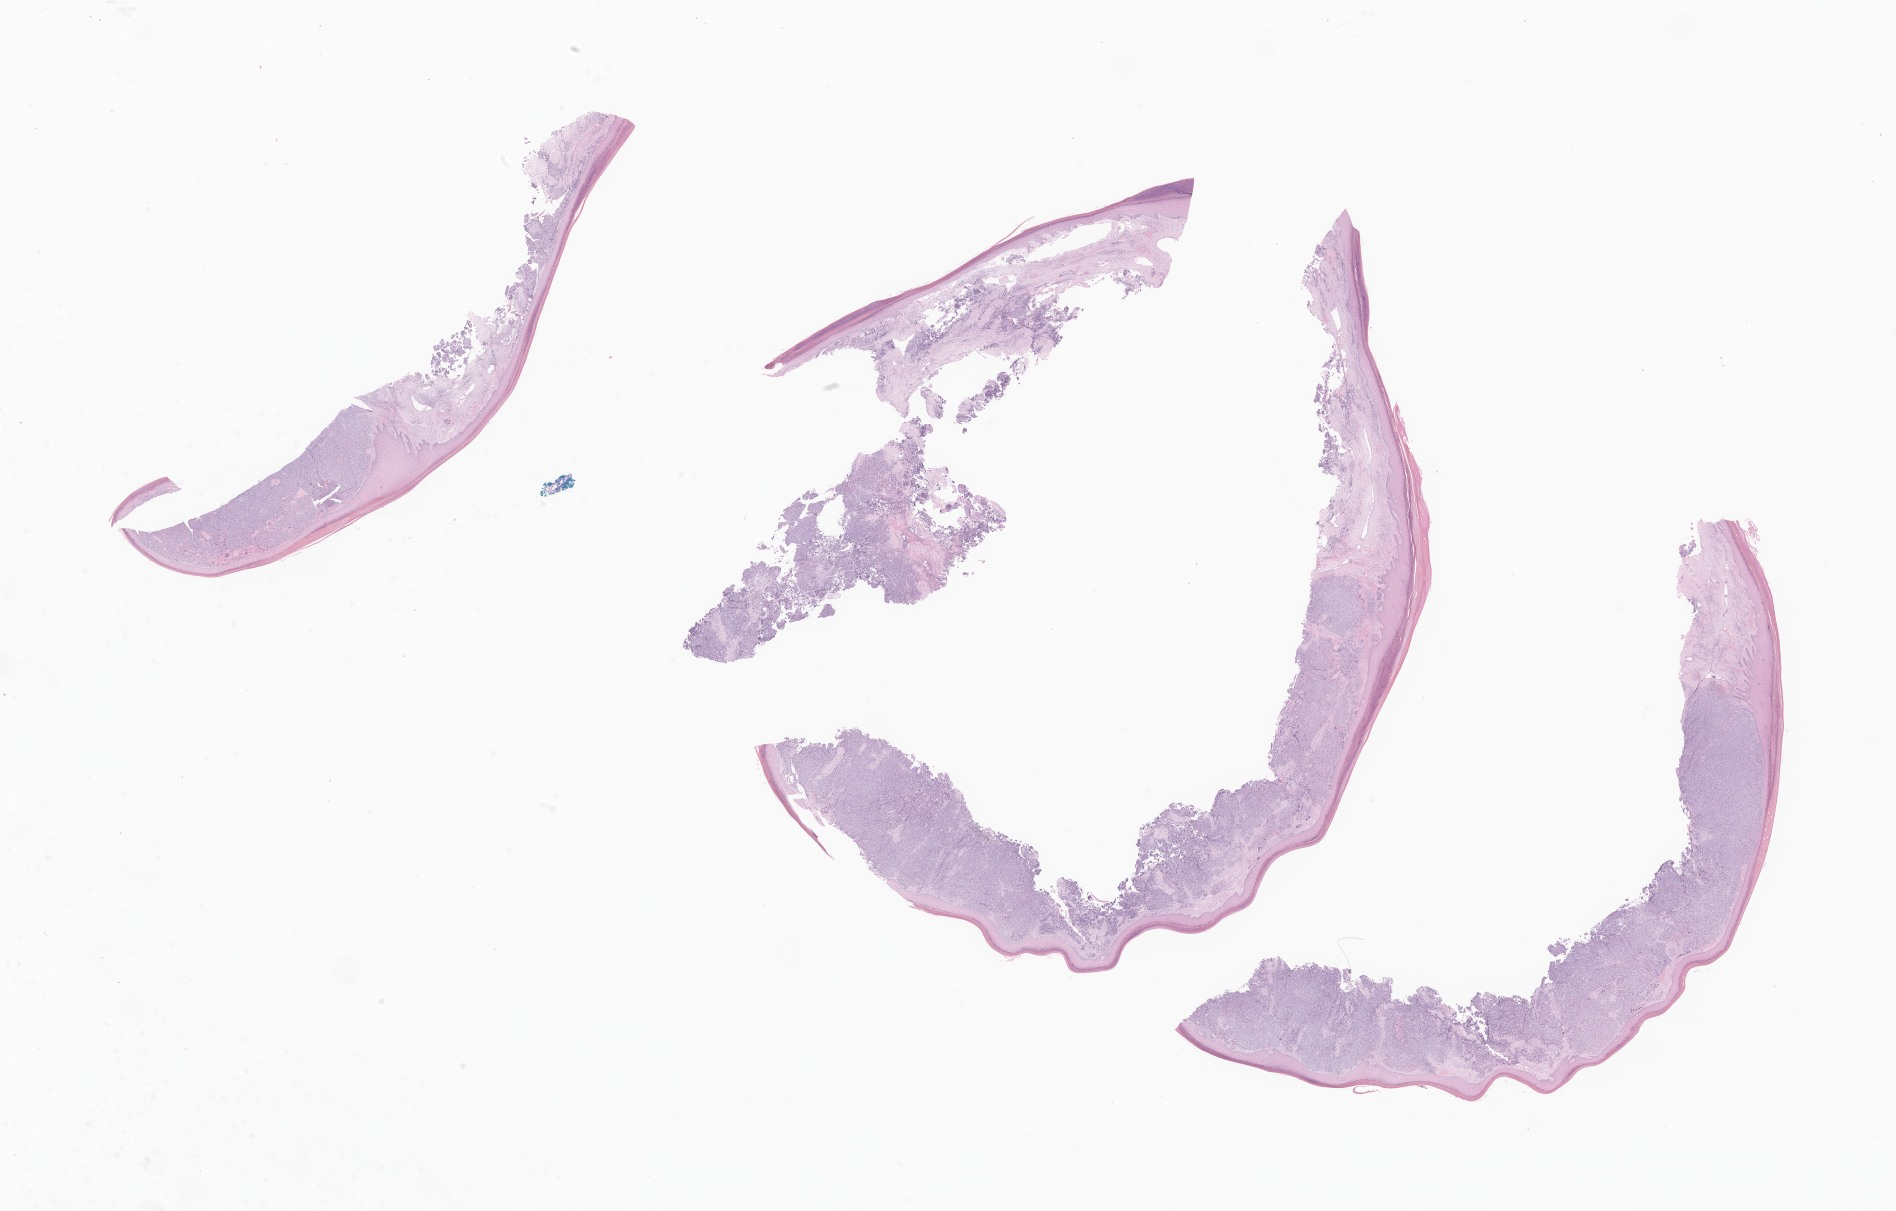
Digitized haematoxylin and eosin-stained section of tumor tissue from the soft tissue of lower extremity, whole scanned area (about 32.0 x 20.4 mm) shown as a low-resolution overview, formalin-fixed paraffin-embedded section. Male patient, age 208 months (17 years 4 months).
Diagnosis: Undifferentiated sarcoma.